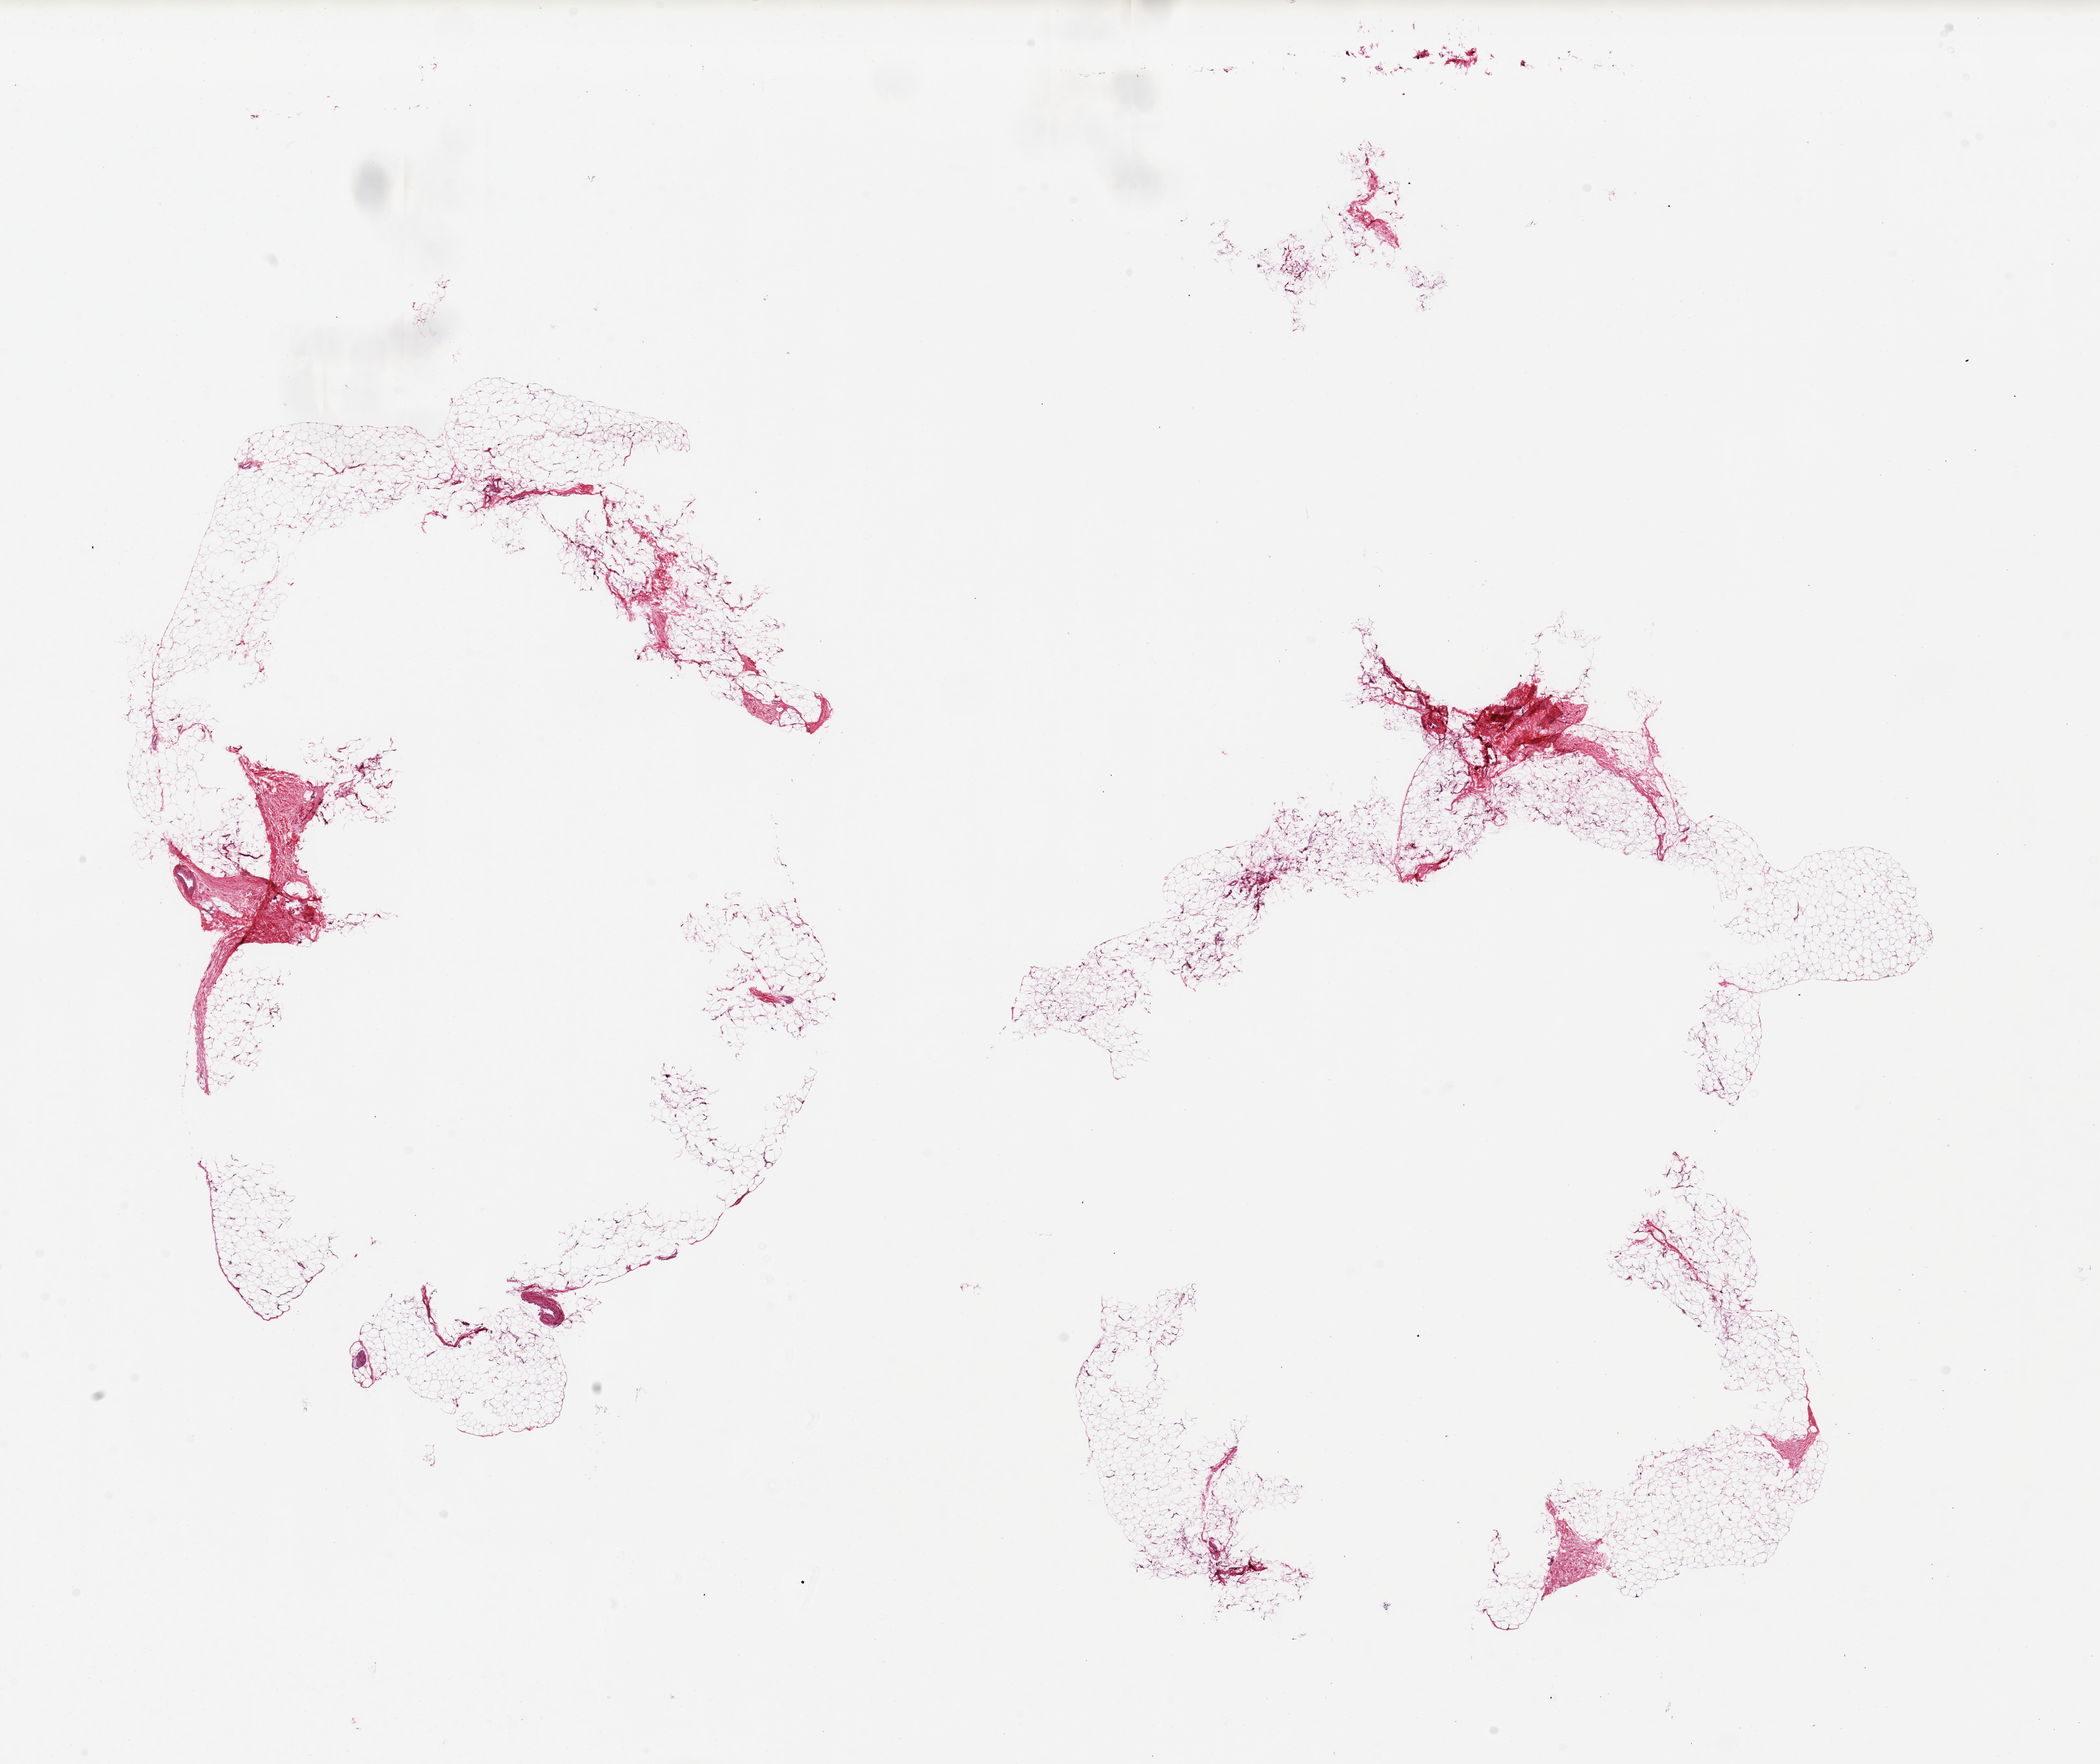
H&E whole-slide image, brightfield — low-resolution overview of the scanned area, about 25.6 x 21.5 mm (slide scanned at 20x); PAXgene-fixed, paraffin-embedded tissue; sampled site (target tissue): adipose tissue; tissue donor sample. Donor: female.
• reviewer comment on this tissue sample: 2 pieces ~10x9mm